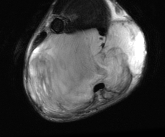
MRI of an extremity soft-tissue mass, one axial slice. Slice 22 of 81 in the series (ordered by position). T2-weighted fat-saturated. MR volume resampled by the dataset authors to the PET/CT grid (not the native acquisition matrix). 3.27 mm slice thickness. 165 × 137 image matrix. Male patient. Case-level facts recorded for this patient, not image findings: histological type: liposarcoma - round cell; grade: high; site of the primary tumour: right calf.
Structures marked on this image (expert contour drawn on MRI and transferred to this co-registered scan by the dataset authors):
- gross tumour volume (mass): bounding box [x1, y1, x2, y2] px = [28, 20, 145, 115]